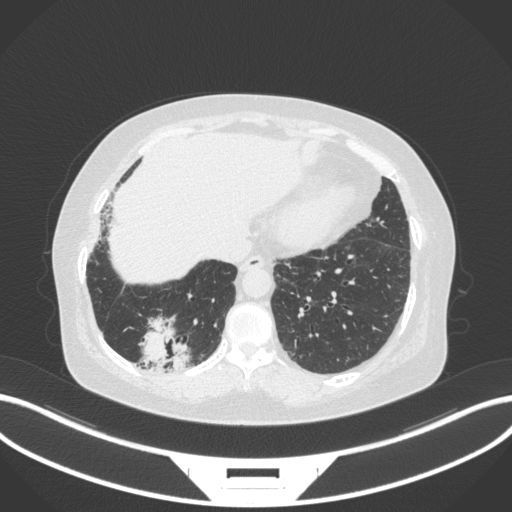
Chest CT, one axial slice. Position 42 of 303 along the scan axis. 120 kVp. Lung window (W 1500 / L -600 HU). 1 mm slice thickness. 512 × 512 image matrix, field of view 400 × 400 mm. Patient: female, 65 years. From the clinical record (not read from this slice): clinical TNM (as recorded): T2b N1 M0; histopathological grade: G1.
Annotated regions visible in this slice (rectangle marked by the reading radiologist):
- lung tumour (recorded histology: adenocarcinoma): box from (x=133, y=312) to (x=193, y=374) px